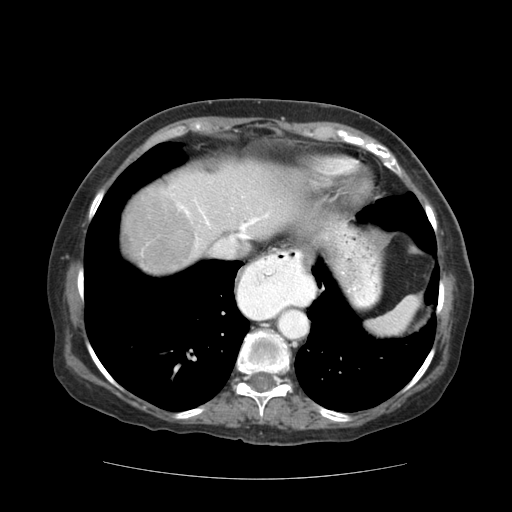
Contrast-enhanced abdominal CT (liver protocol), one axial slice. Position 95 of 111 along the scan axis. Soft-tissue window (W 400 / L 40 HU). 2.5 mm slice thickness. 512 × 512 image matrix, field of view 360 × 360 mm. From the clinical record (not read from this slice): diagnosis: hepatocellular carcinoma (patient treated with transarterial chemoembolisation; whether this scan precedes or follows treatment is not stated here); TNM stage (as recorded): Stage-I; Child-Pugh class: A; tumour nodularity: uninodular; tumour size: 7.3 cm.
Outlined on this slice (semi-automatically segmented with operator editing):
- abdominal aorta: bounding box <278,309,307,338> (left, top, right, bottom; pixels)
- liver parenchyma outside the tumour (the mass and vessels are separate outlines, so this box may not span the whole liver): <122,162,302,274>
- mass: <125,194,193,270>
- liver vessels: <177,196,269,247>